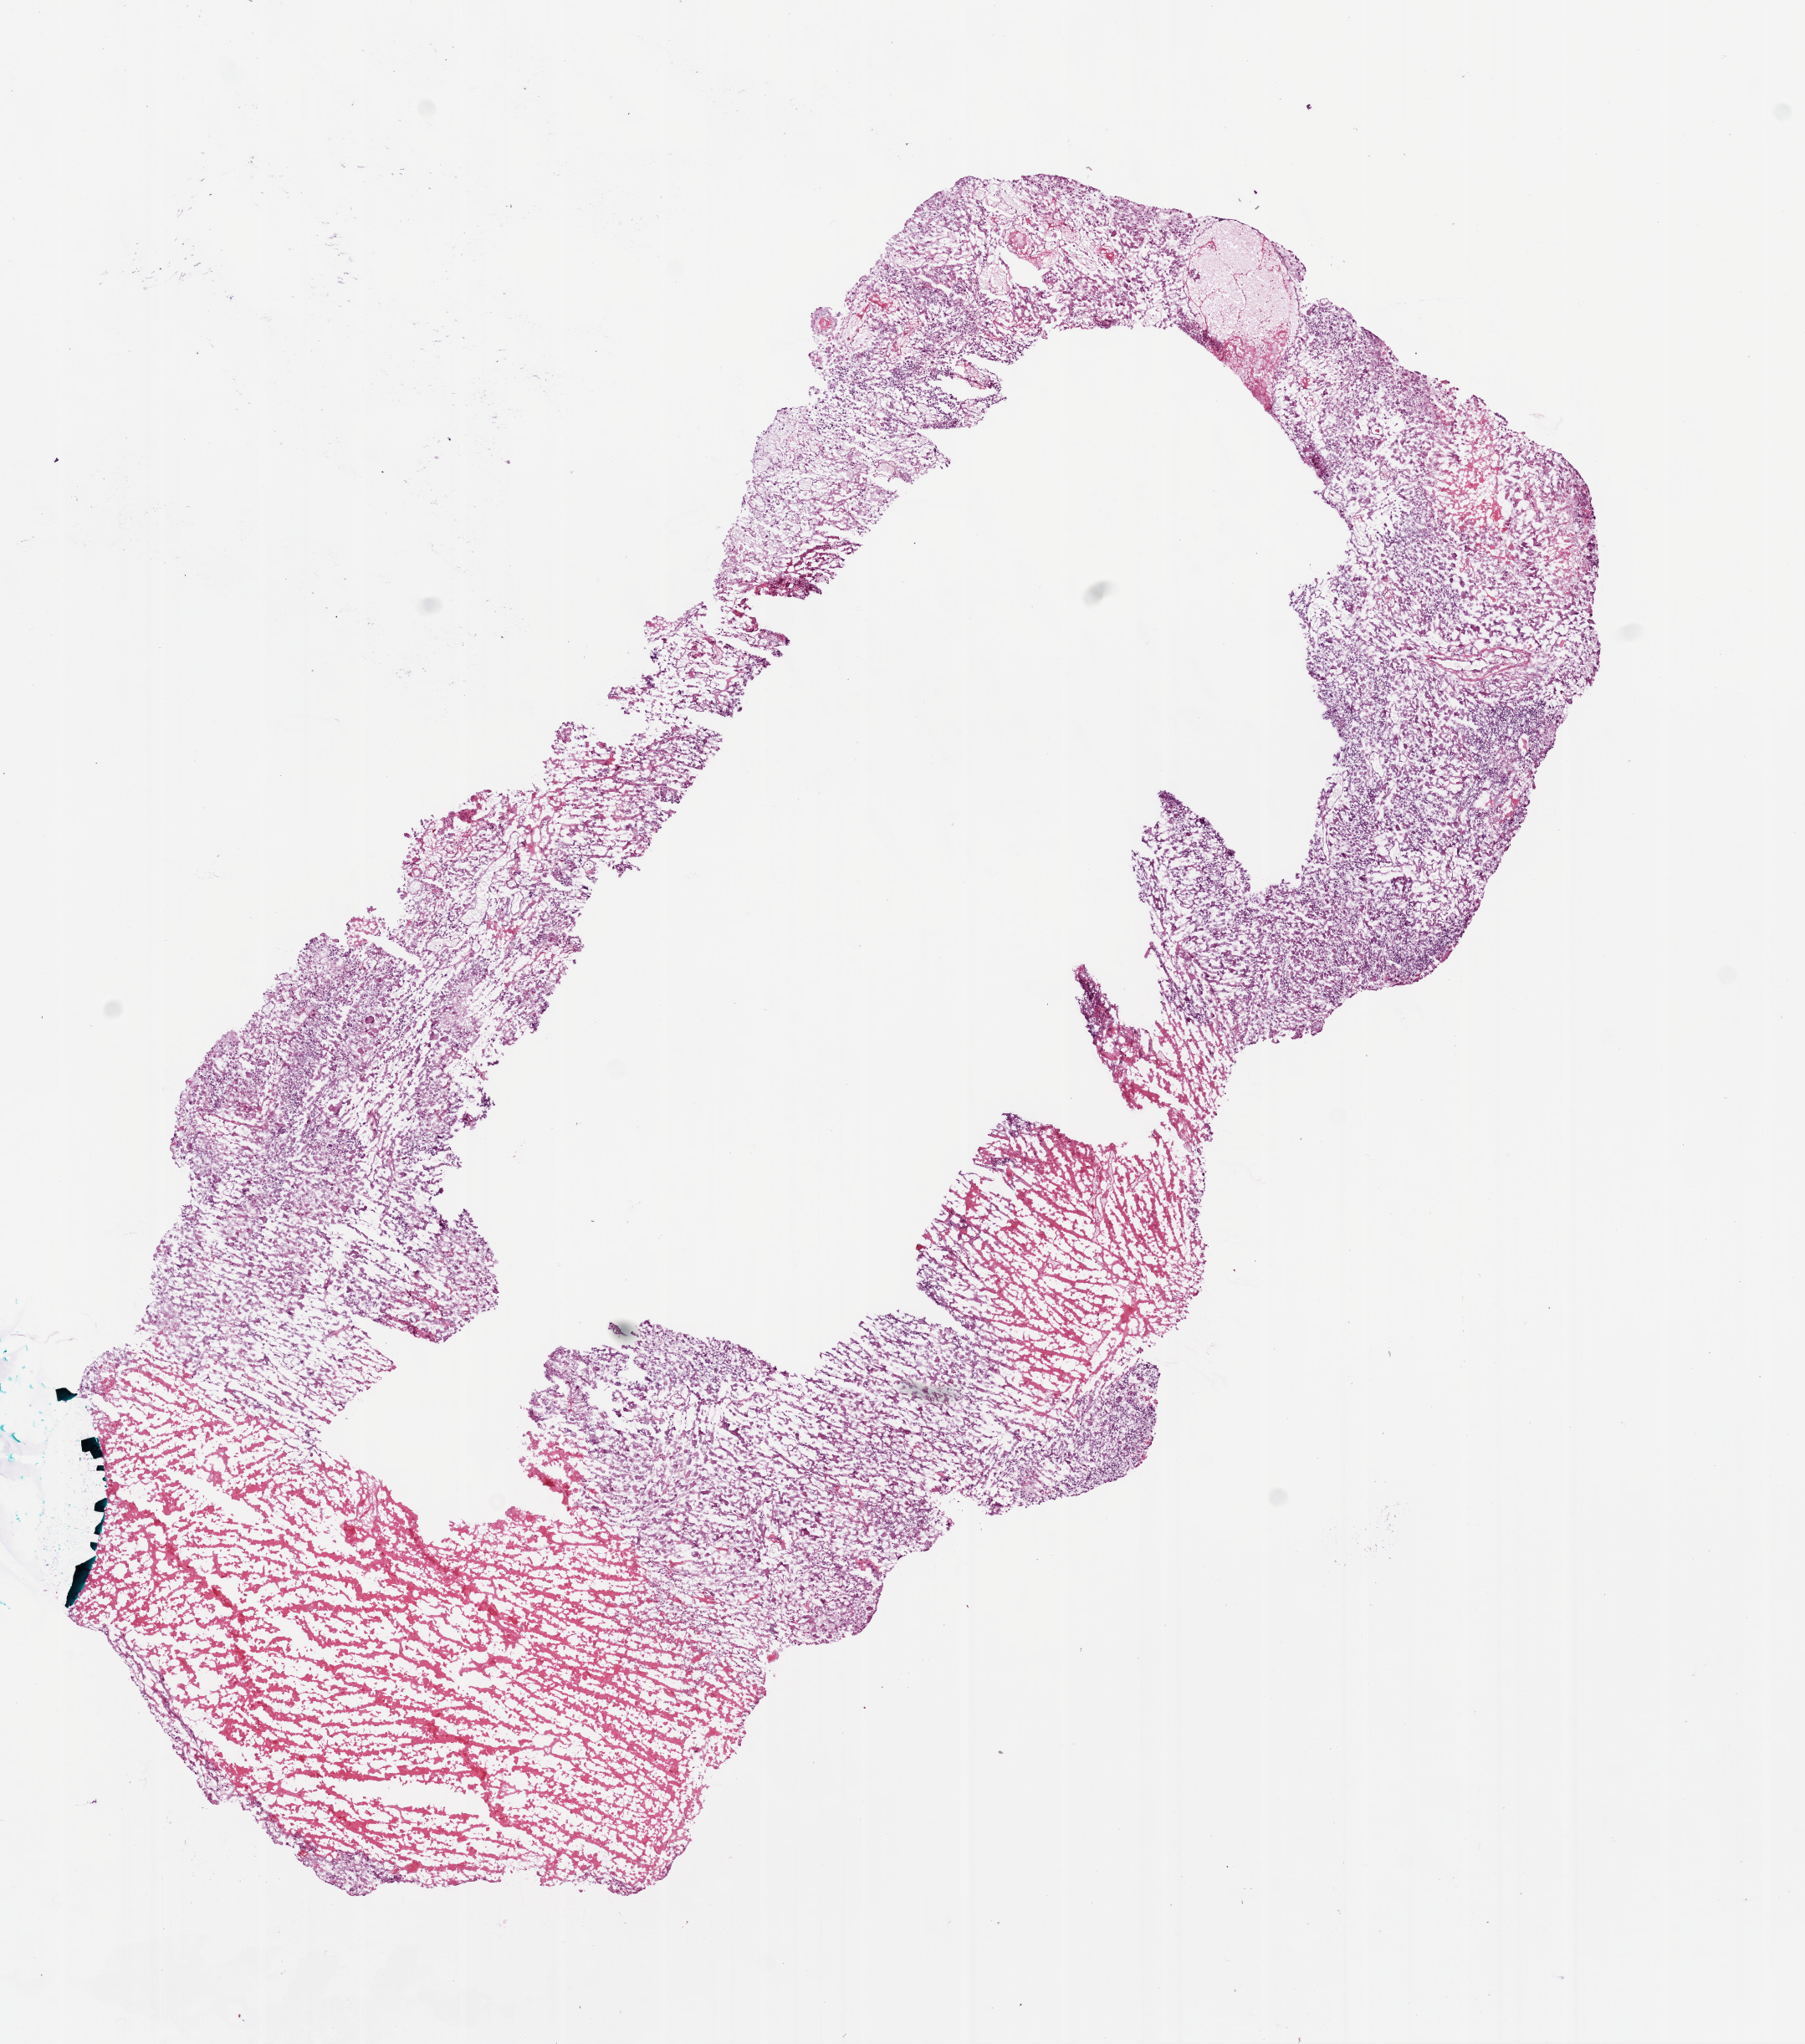
Whole-slide histology image, H&E-stained — a low-resolution overview of the entire scanned area, about 8.7 x 9.9 mm (slide scanned at 20x). Frozen section. Sample: primary tumour, brain. Patient: male, age at initial diagnosis 24 years. Slide review estimates, as recorded: tumour cells 60%, tumour nuclei 100%, normal cells 0%, stromal cells 0%, necrosis 40%.
Histologic diagnosis: Glioblastoma.